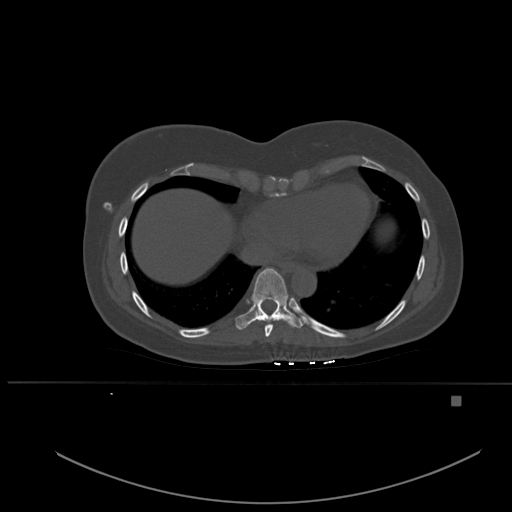
CT including the spine, one axial slice; slice 309 of 651 in the series (ordered by position); bone window (W 1800 / L 400 HU); 1.5 mm slice thickness; 512 × 512 image matrix, field of view 443 × 443 mm. Female patient, age 49 years. Case-level facts recorded for this patient, not image findings: primary cancer: breast; vertebrae with lytic lesions (as recorded): L3, T12, L4.
Outlined on this slice (semi-automatically segmented with operator editing):
- T8 vertebra: box from (x=265, y=325) to (x=273, y=337) px
- T9 vertebra: (x=235, y=268)–(x=303, y=330)